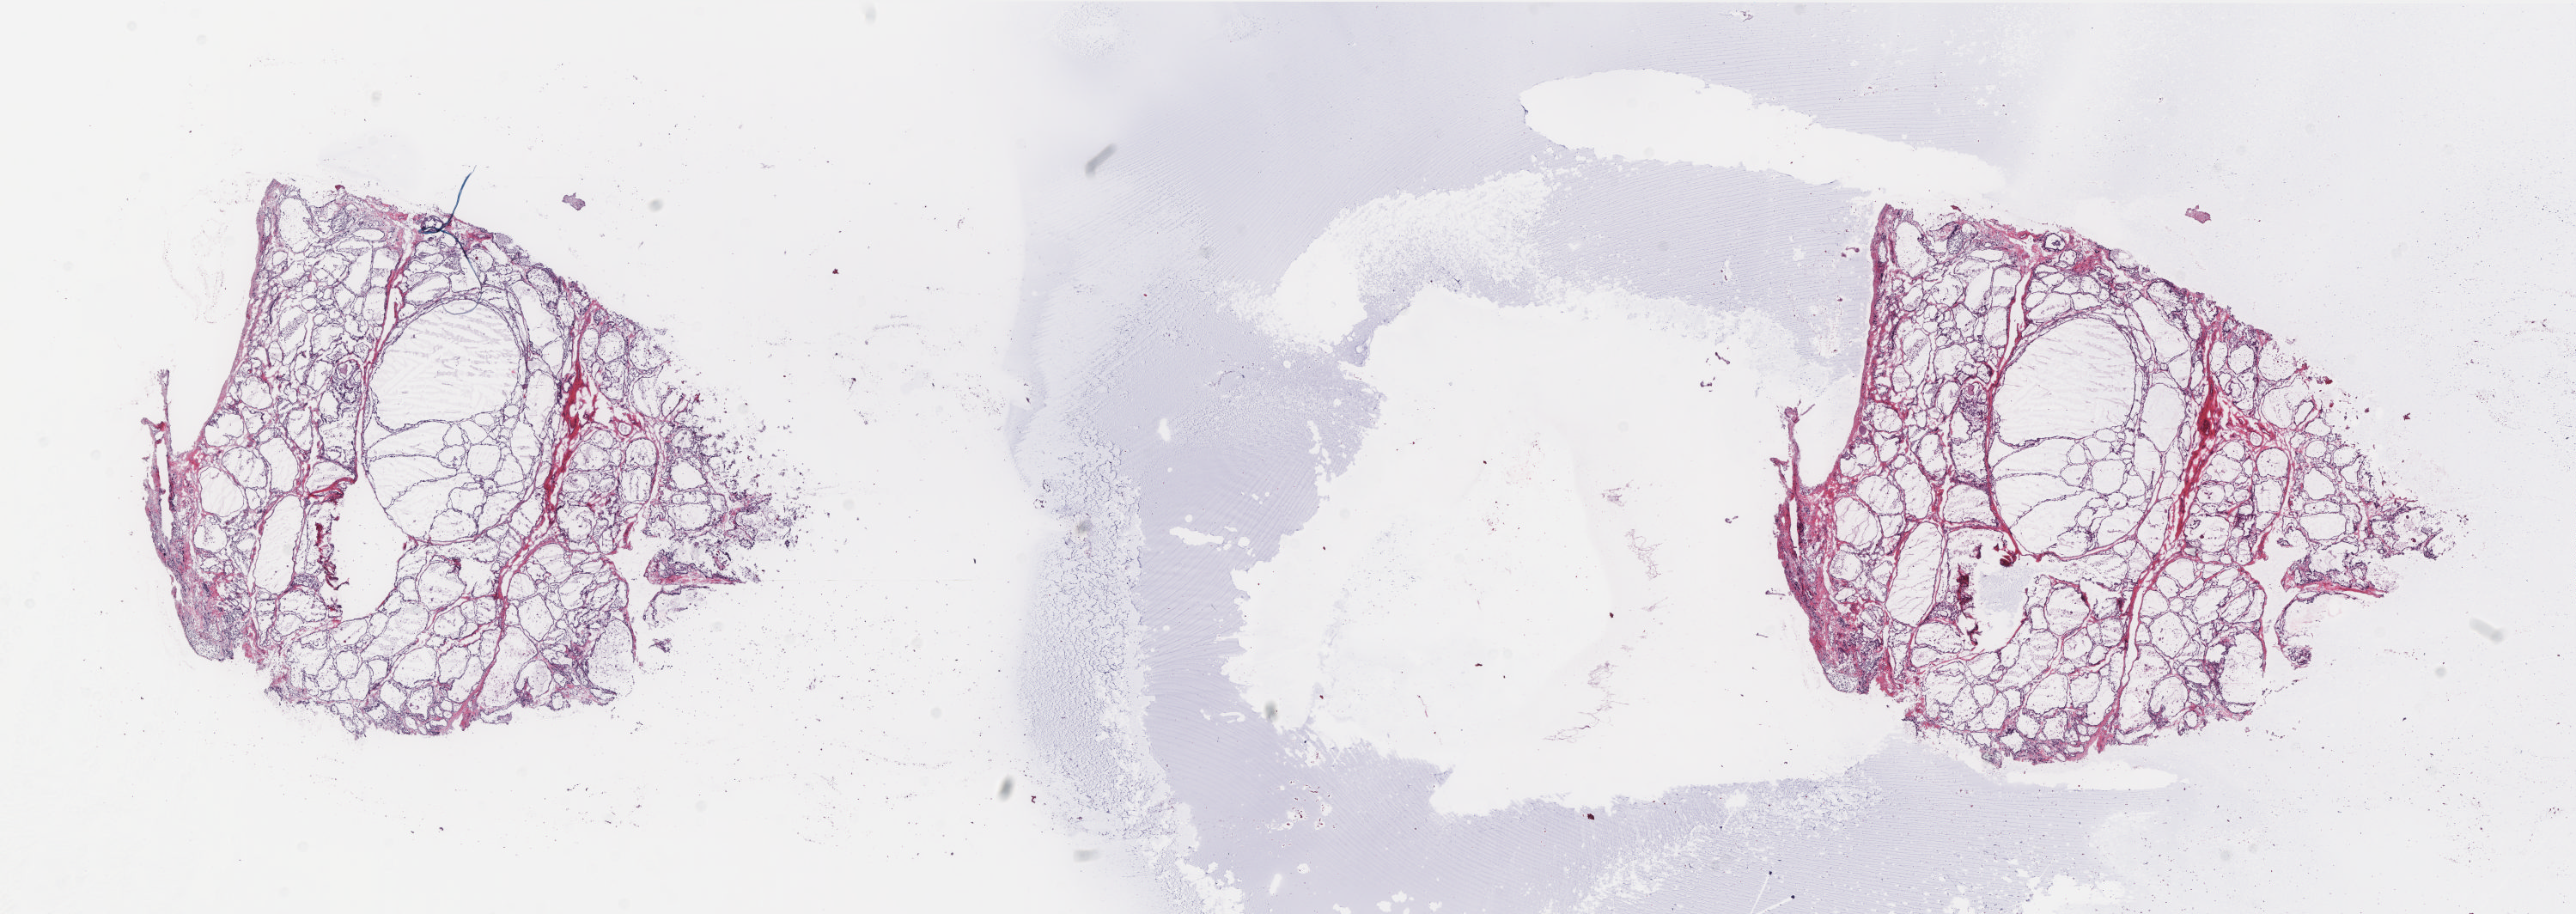
H&E whole-slide image, low-resolution overview of the scanned area, about 24.0 x 8.5 mm. Frozen section from the top of the tissue portion. Sample: solid tissue normal (non-tumour tissue), thyroid. Patient: male, age at initial diagnosis 58 years. Composition of this section per pathologist review: tumour cells 0%, tumour nuclei 0%, normal cells 100%, stromal cells 0%, necrosis 0%. Inflammatory infiltration, as recorded: lymphocyte infiltration 2%, monocyte infiltration 5%, neutrophil infiltration 0%.
• this section: solid tissue normal sample (biorepository sample class)
• patient diagnosis: Papillary adenocarcinoma, NOS